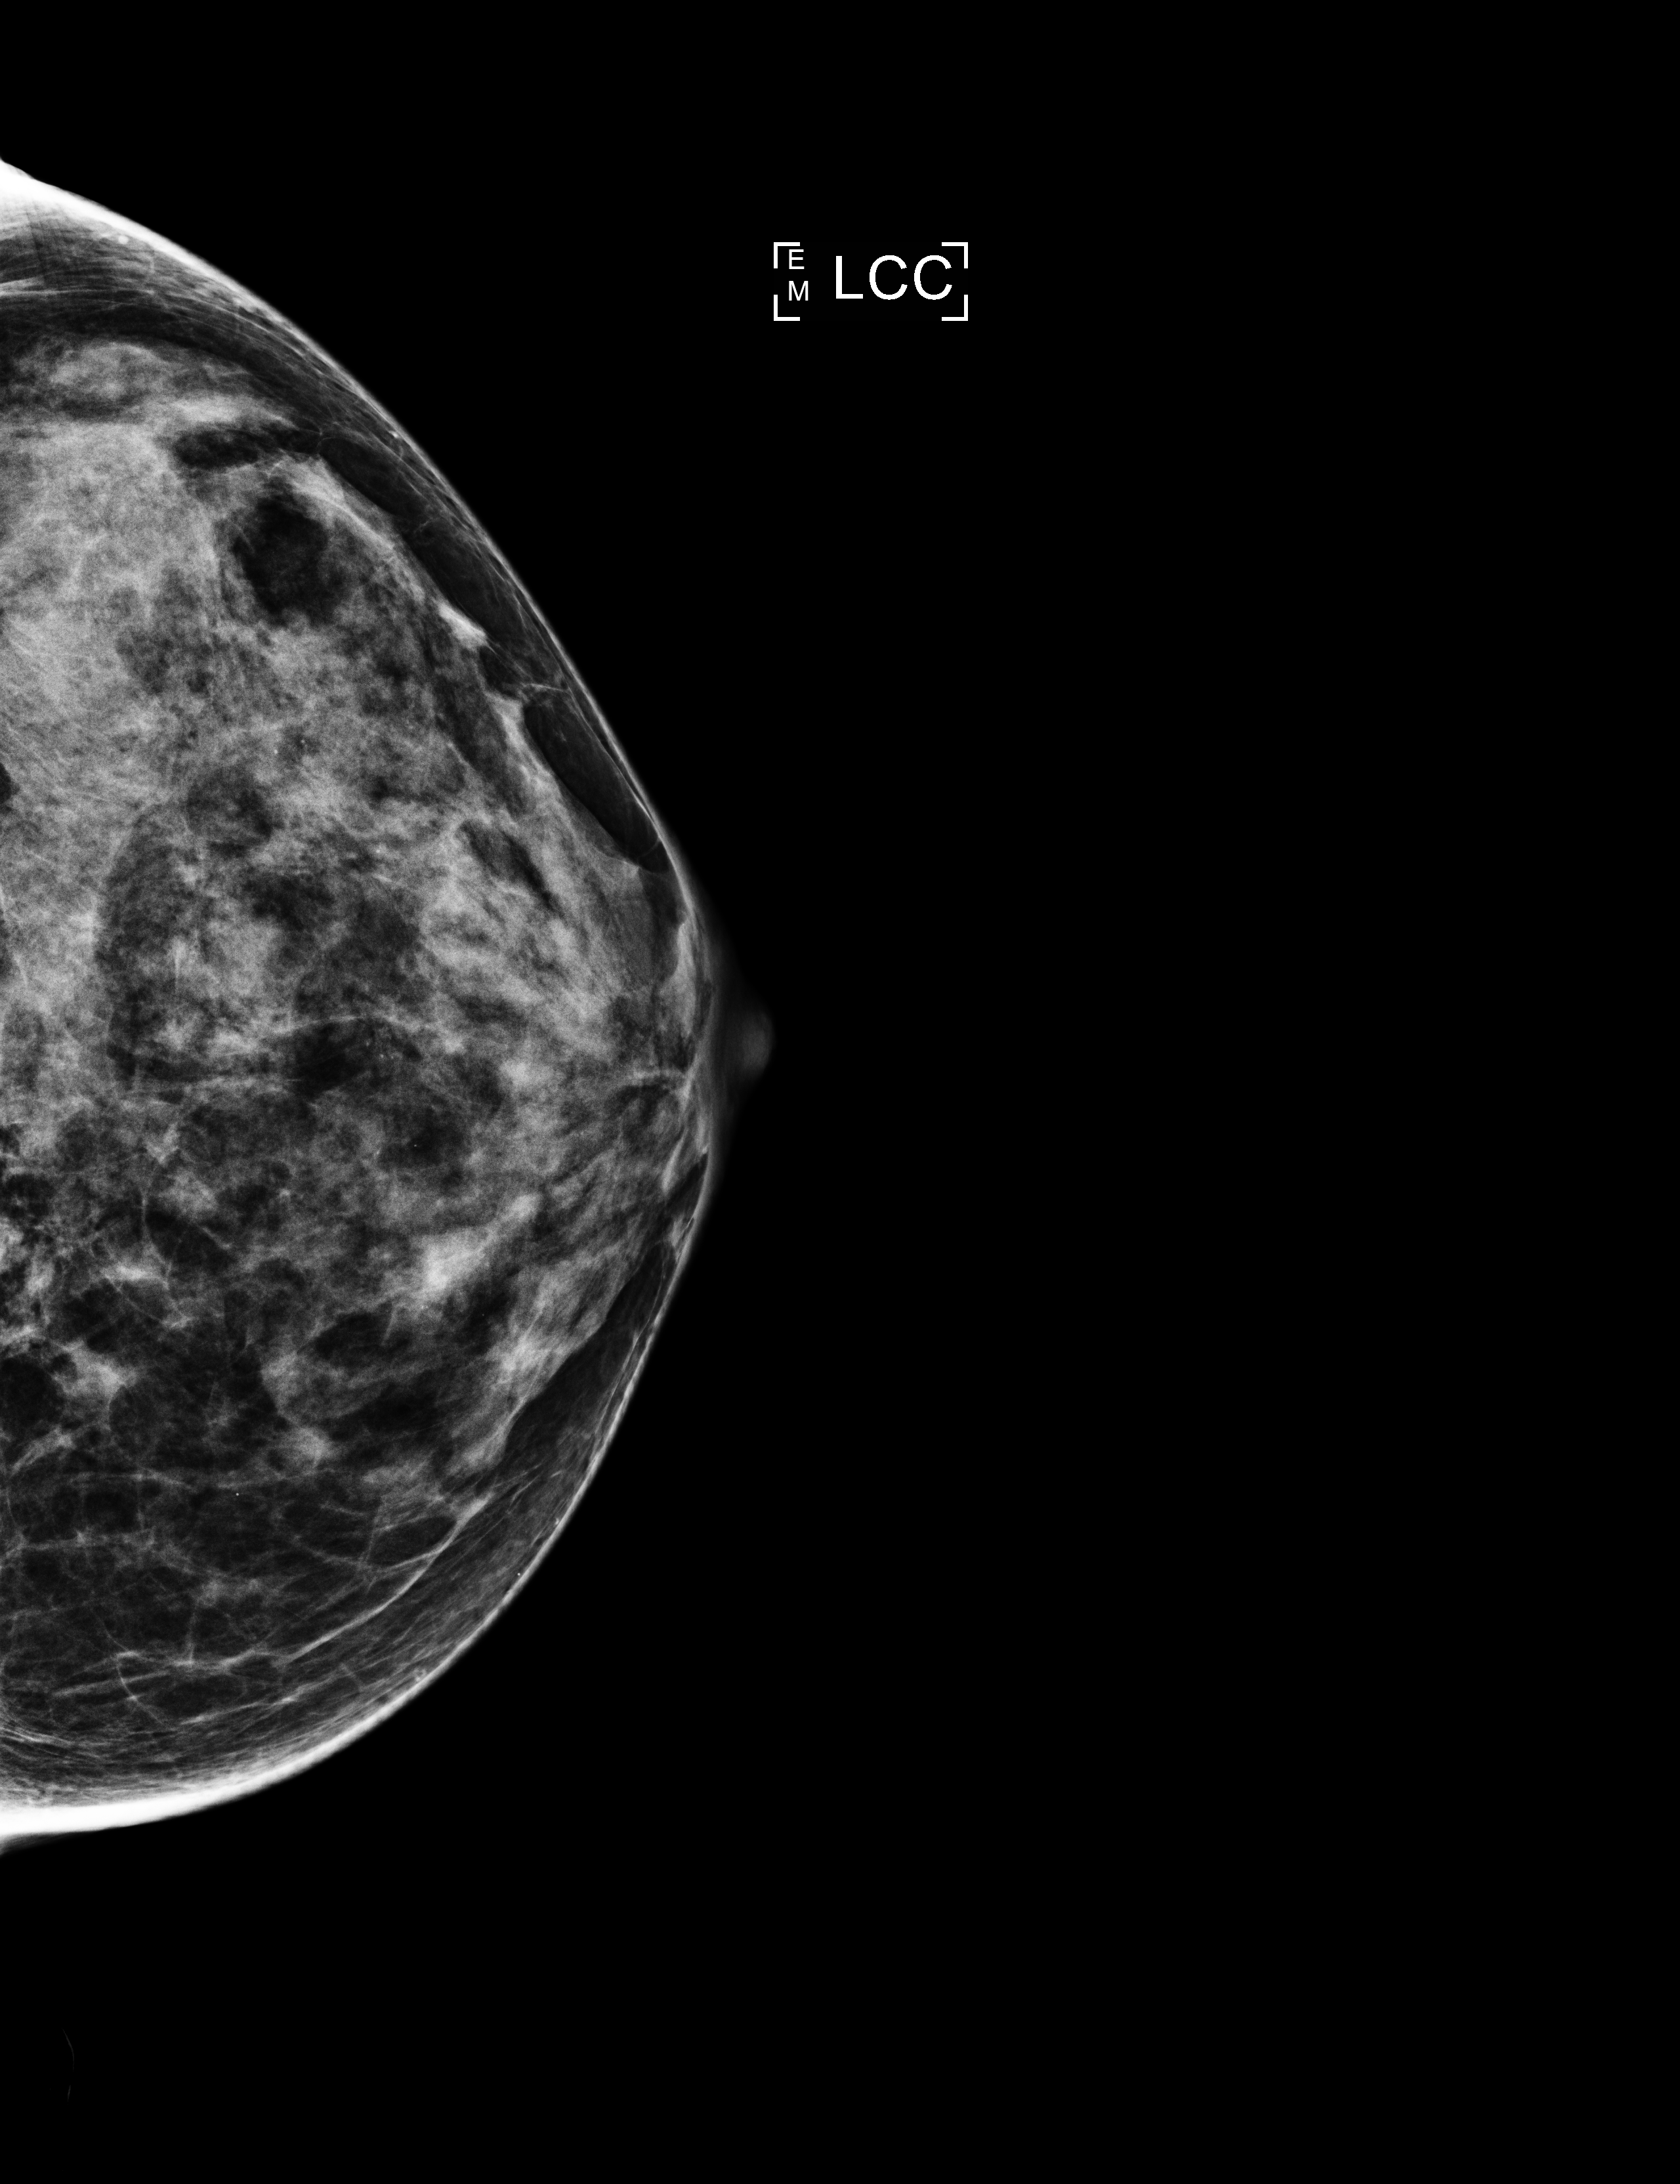
Full-field digital mammogram (FFDM), left breast, cranio-caudal projection, annual screening mammography examination, compressed breast thickness 48 mm, system: Selenia Dimensions. Patient aged 46 years (female).
BI-RADS breast density category at the screening exam (both breasts, scale 1–4): 4. Final BI-RADS category for the screening round (tomosynthesis exam, both breasts): category 1. Recall: no recall after this screen.